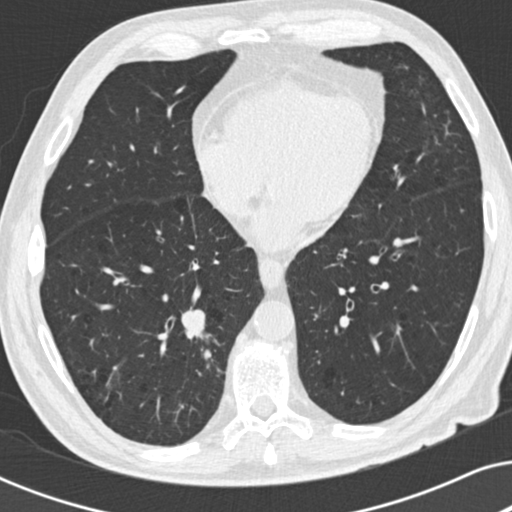
Low-dose screening chest CT, one axial slice. Position 86 of 191 along the scan axis. Lung window (W 1500 / L -600 HU). 2 mm slice thickness. 512 × 512 image matrix, field of view 330 × 330 mm.
Outlined on this slice (expert manual segmentation):
- lesion 1 (tumor, lower lobe of right lung): box from (x=181, y=310) to (x=203, y=339) px